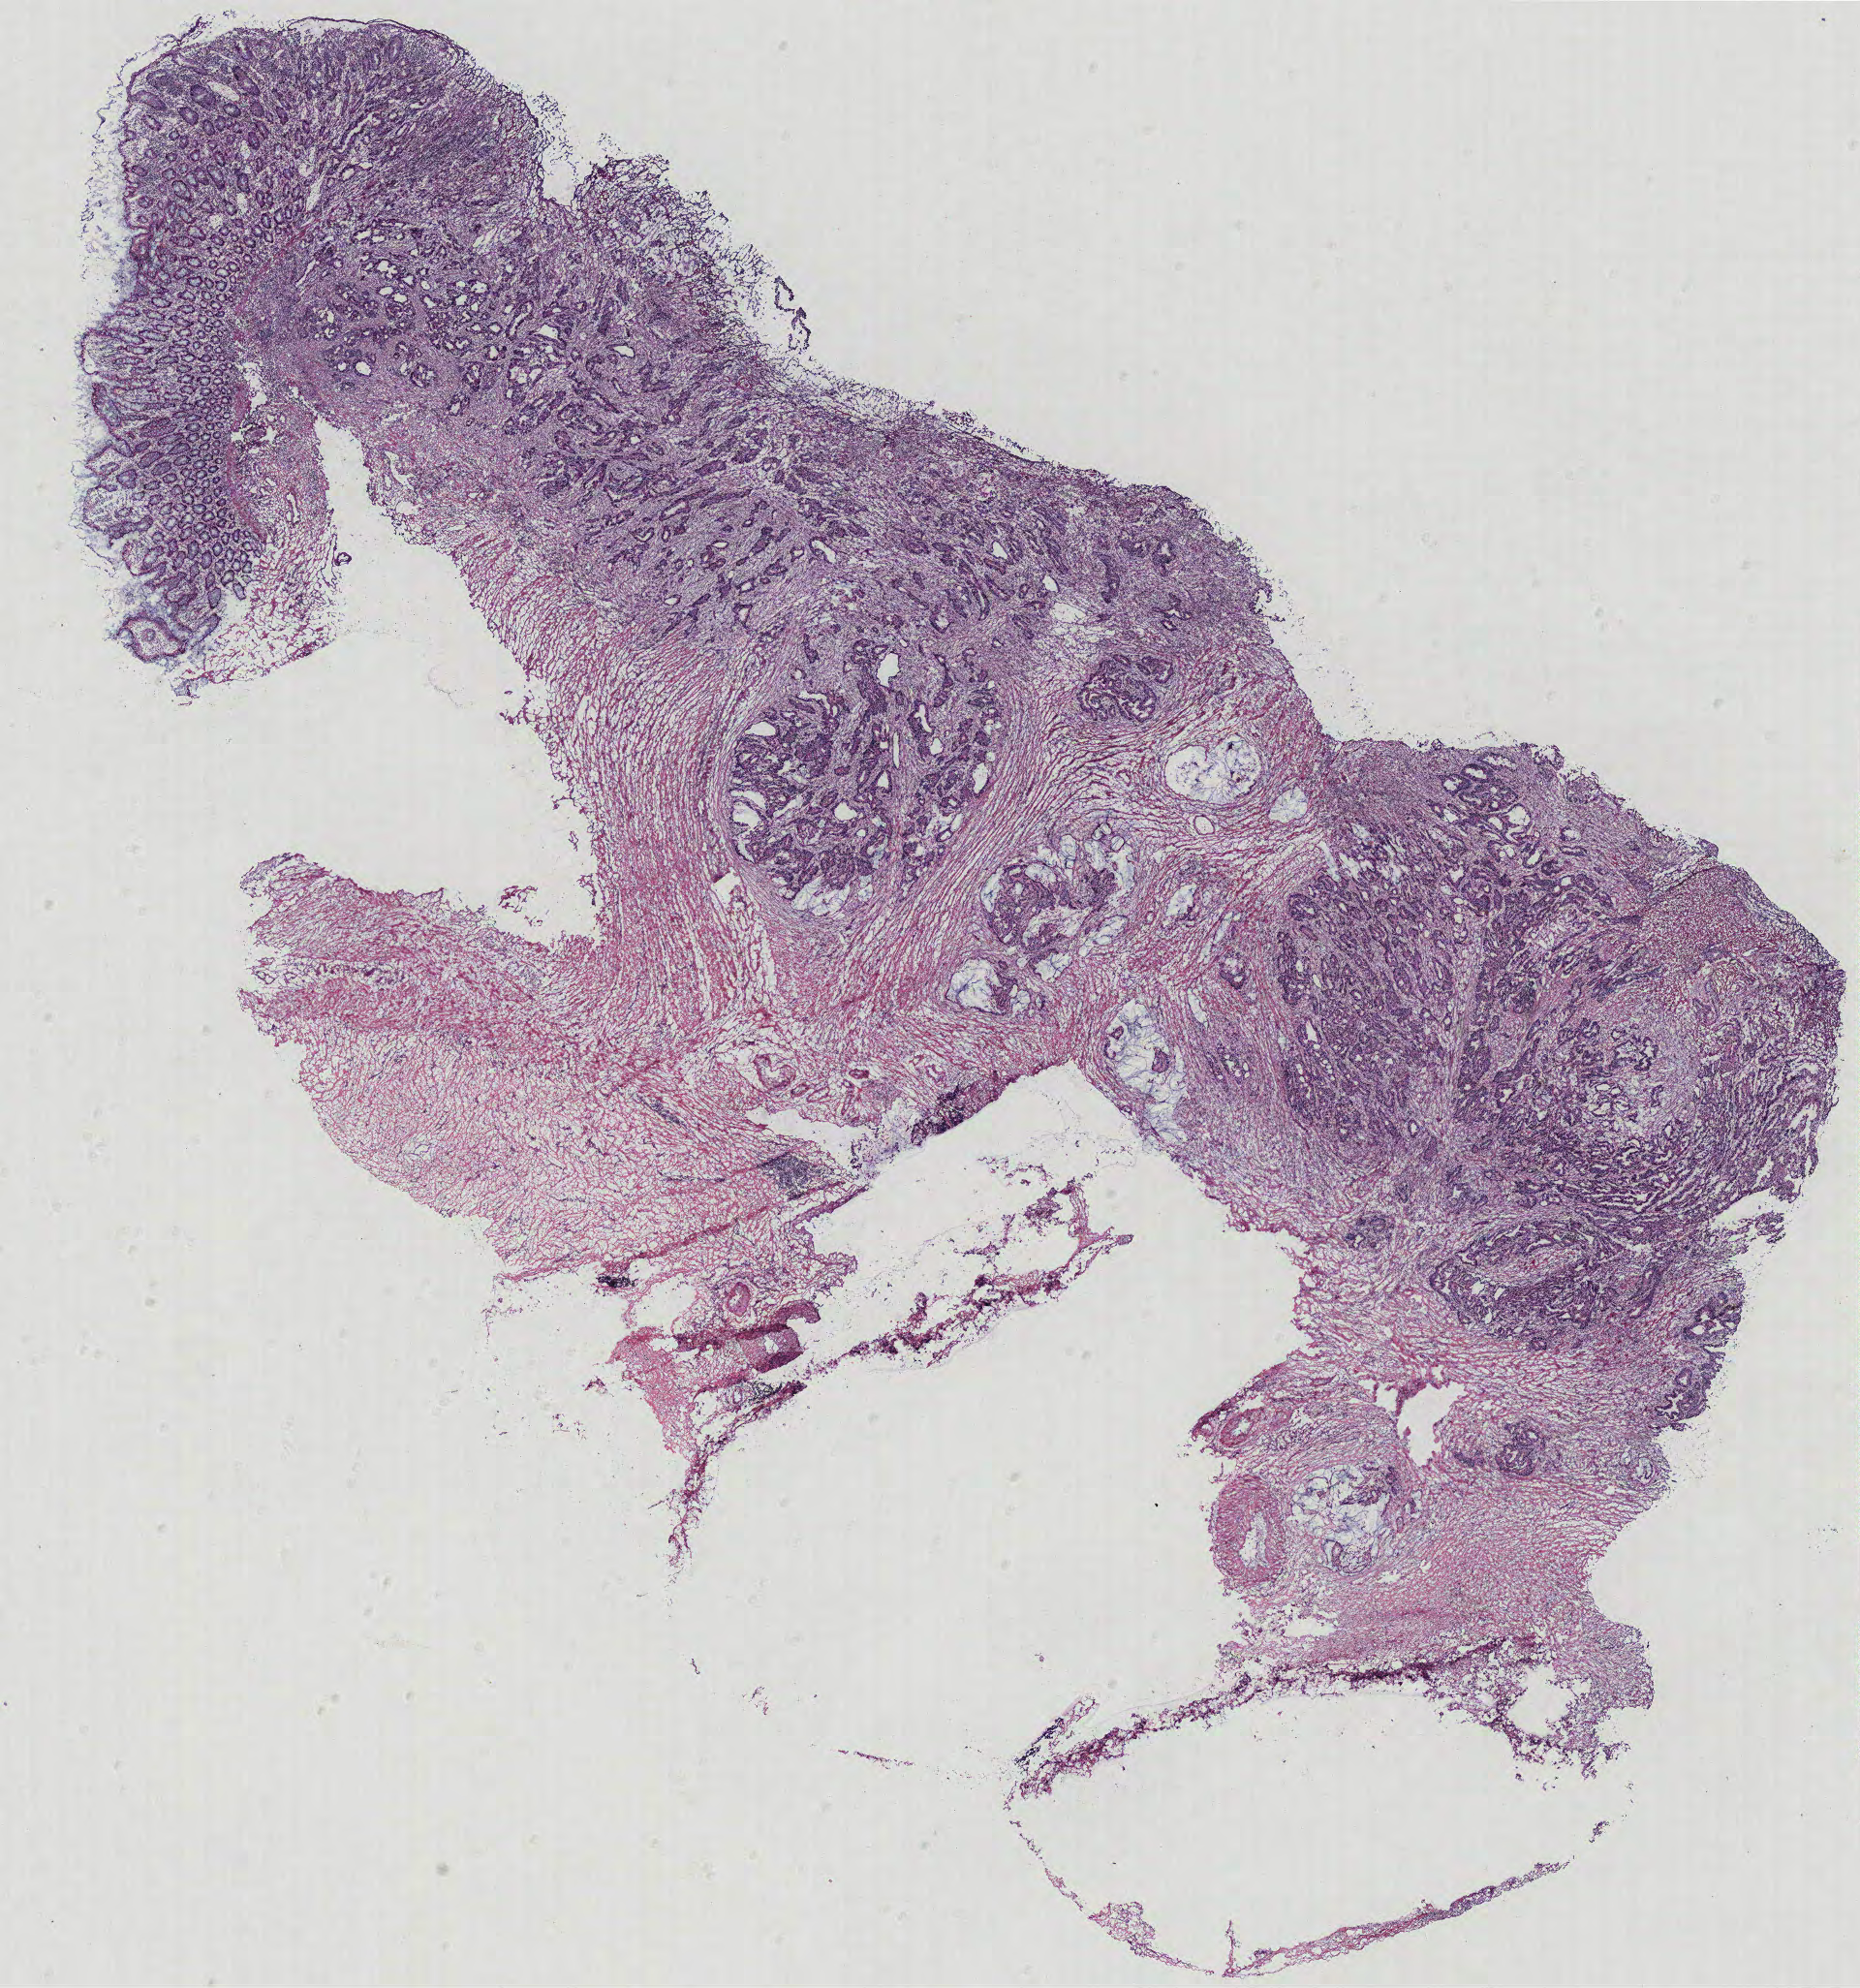
H&E-stained whole-slide image, a low-resolution overview of the entire scanned area, about 15.4 x 16.4 mm (slide scanned at 40x); colon, tissue type not recorded. Patient sex: male.
Patient diagnosis: Adenocarcinoma, NOS.